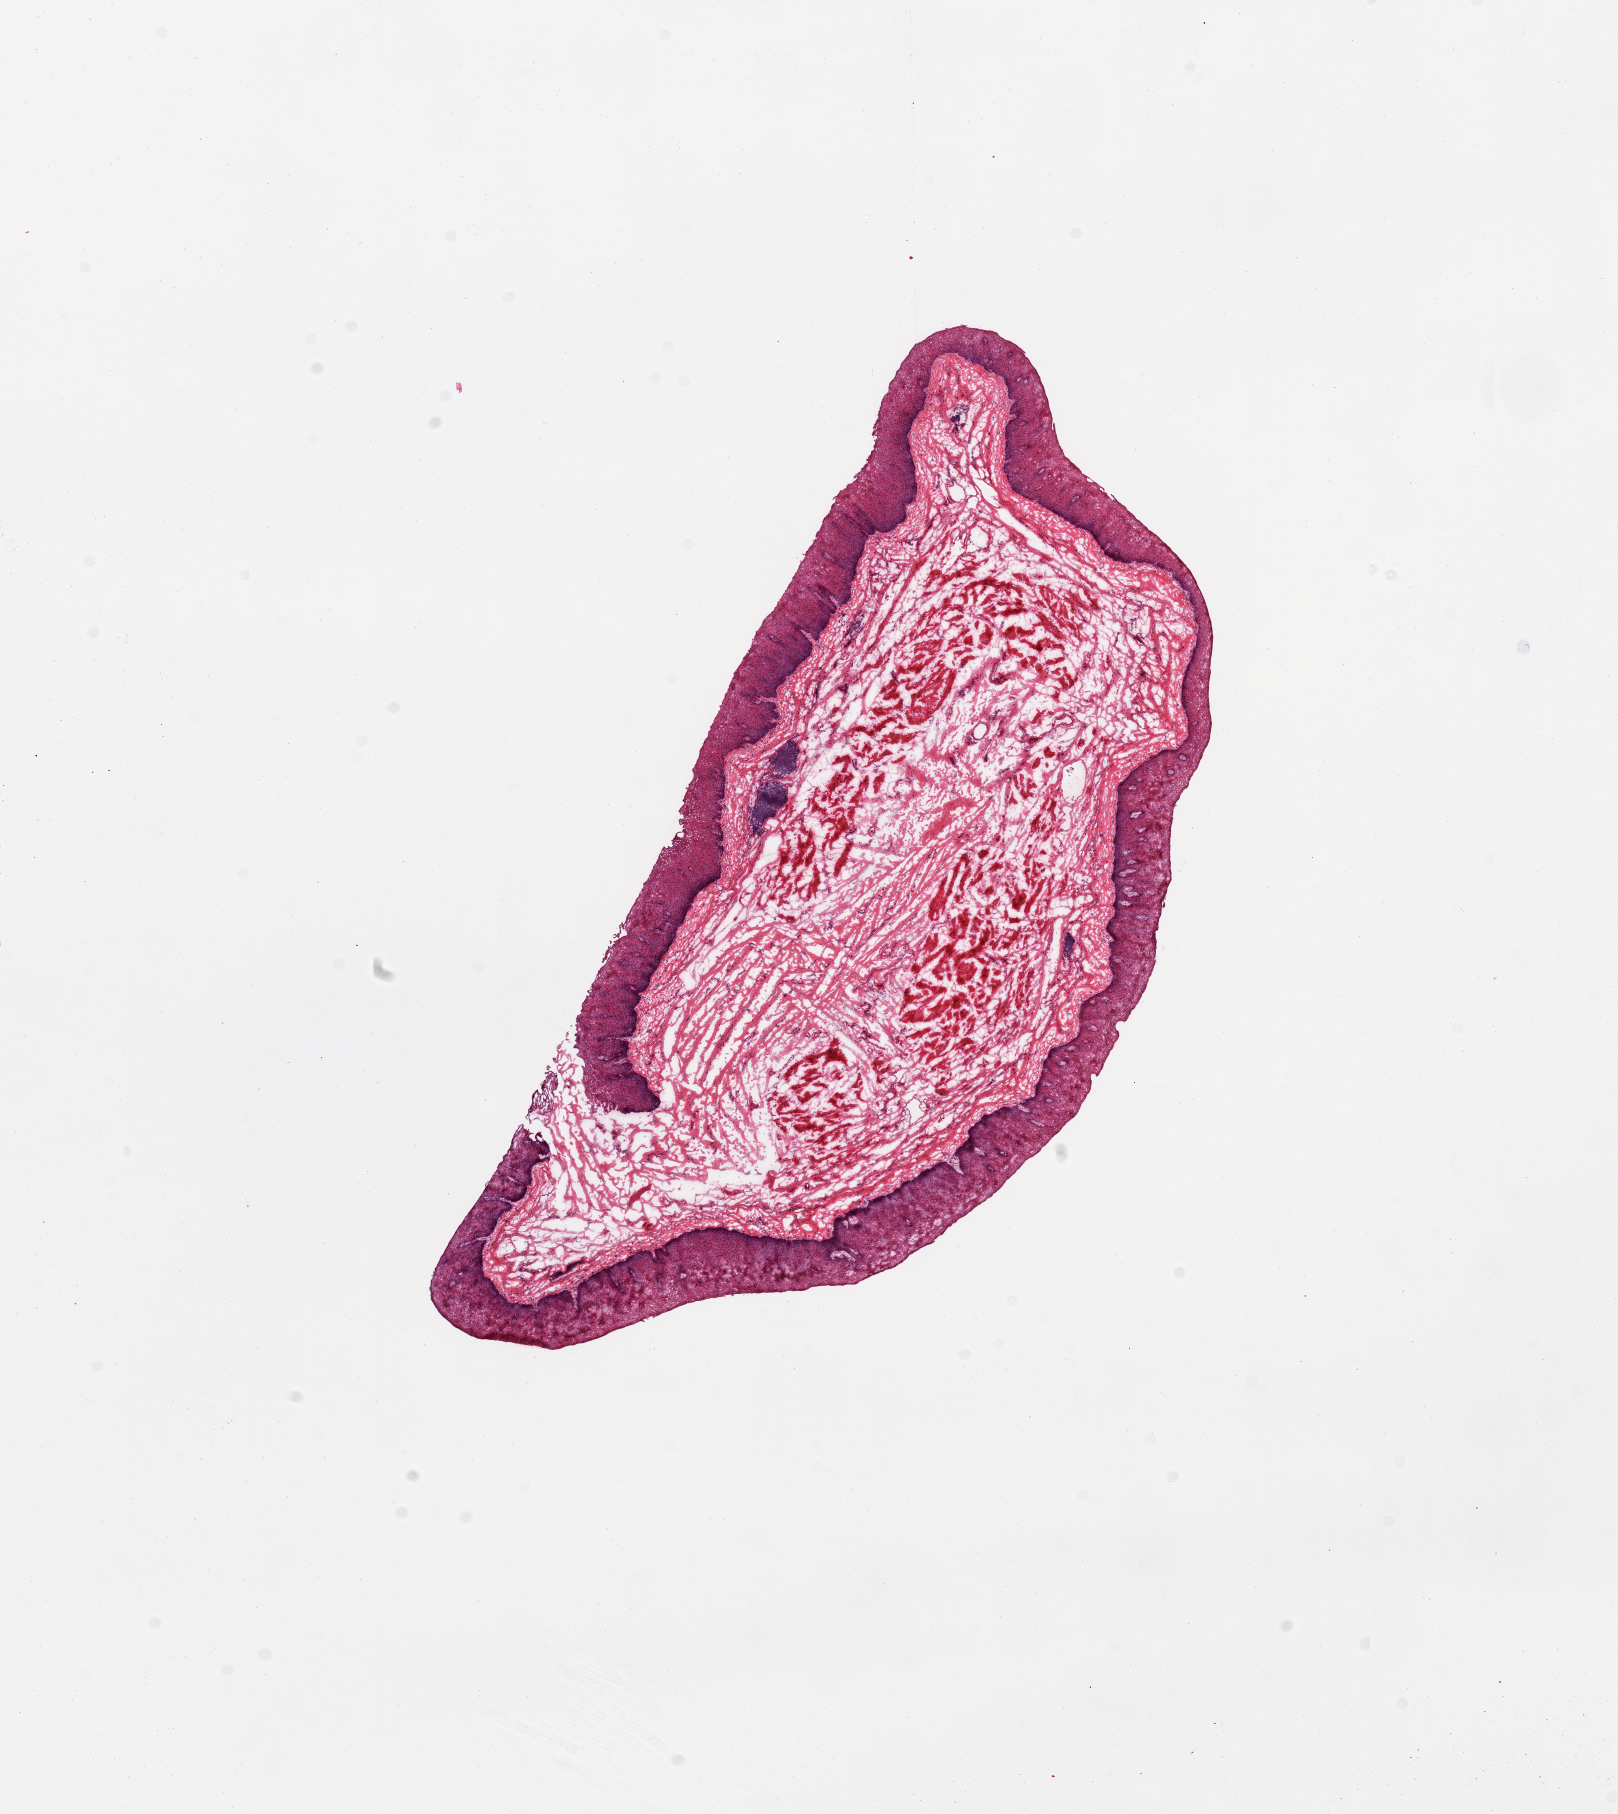
H&E whole-slide image, whole scanned area (about 12.8 x 14.3 mm) shown as a low-resolution overview. Donor sex: female.
Specimen: frozen section (dry ice); target tissue: esophageal mucous membrane; donor tissue sample.